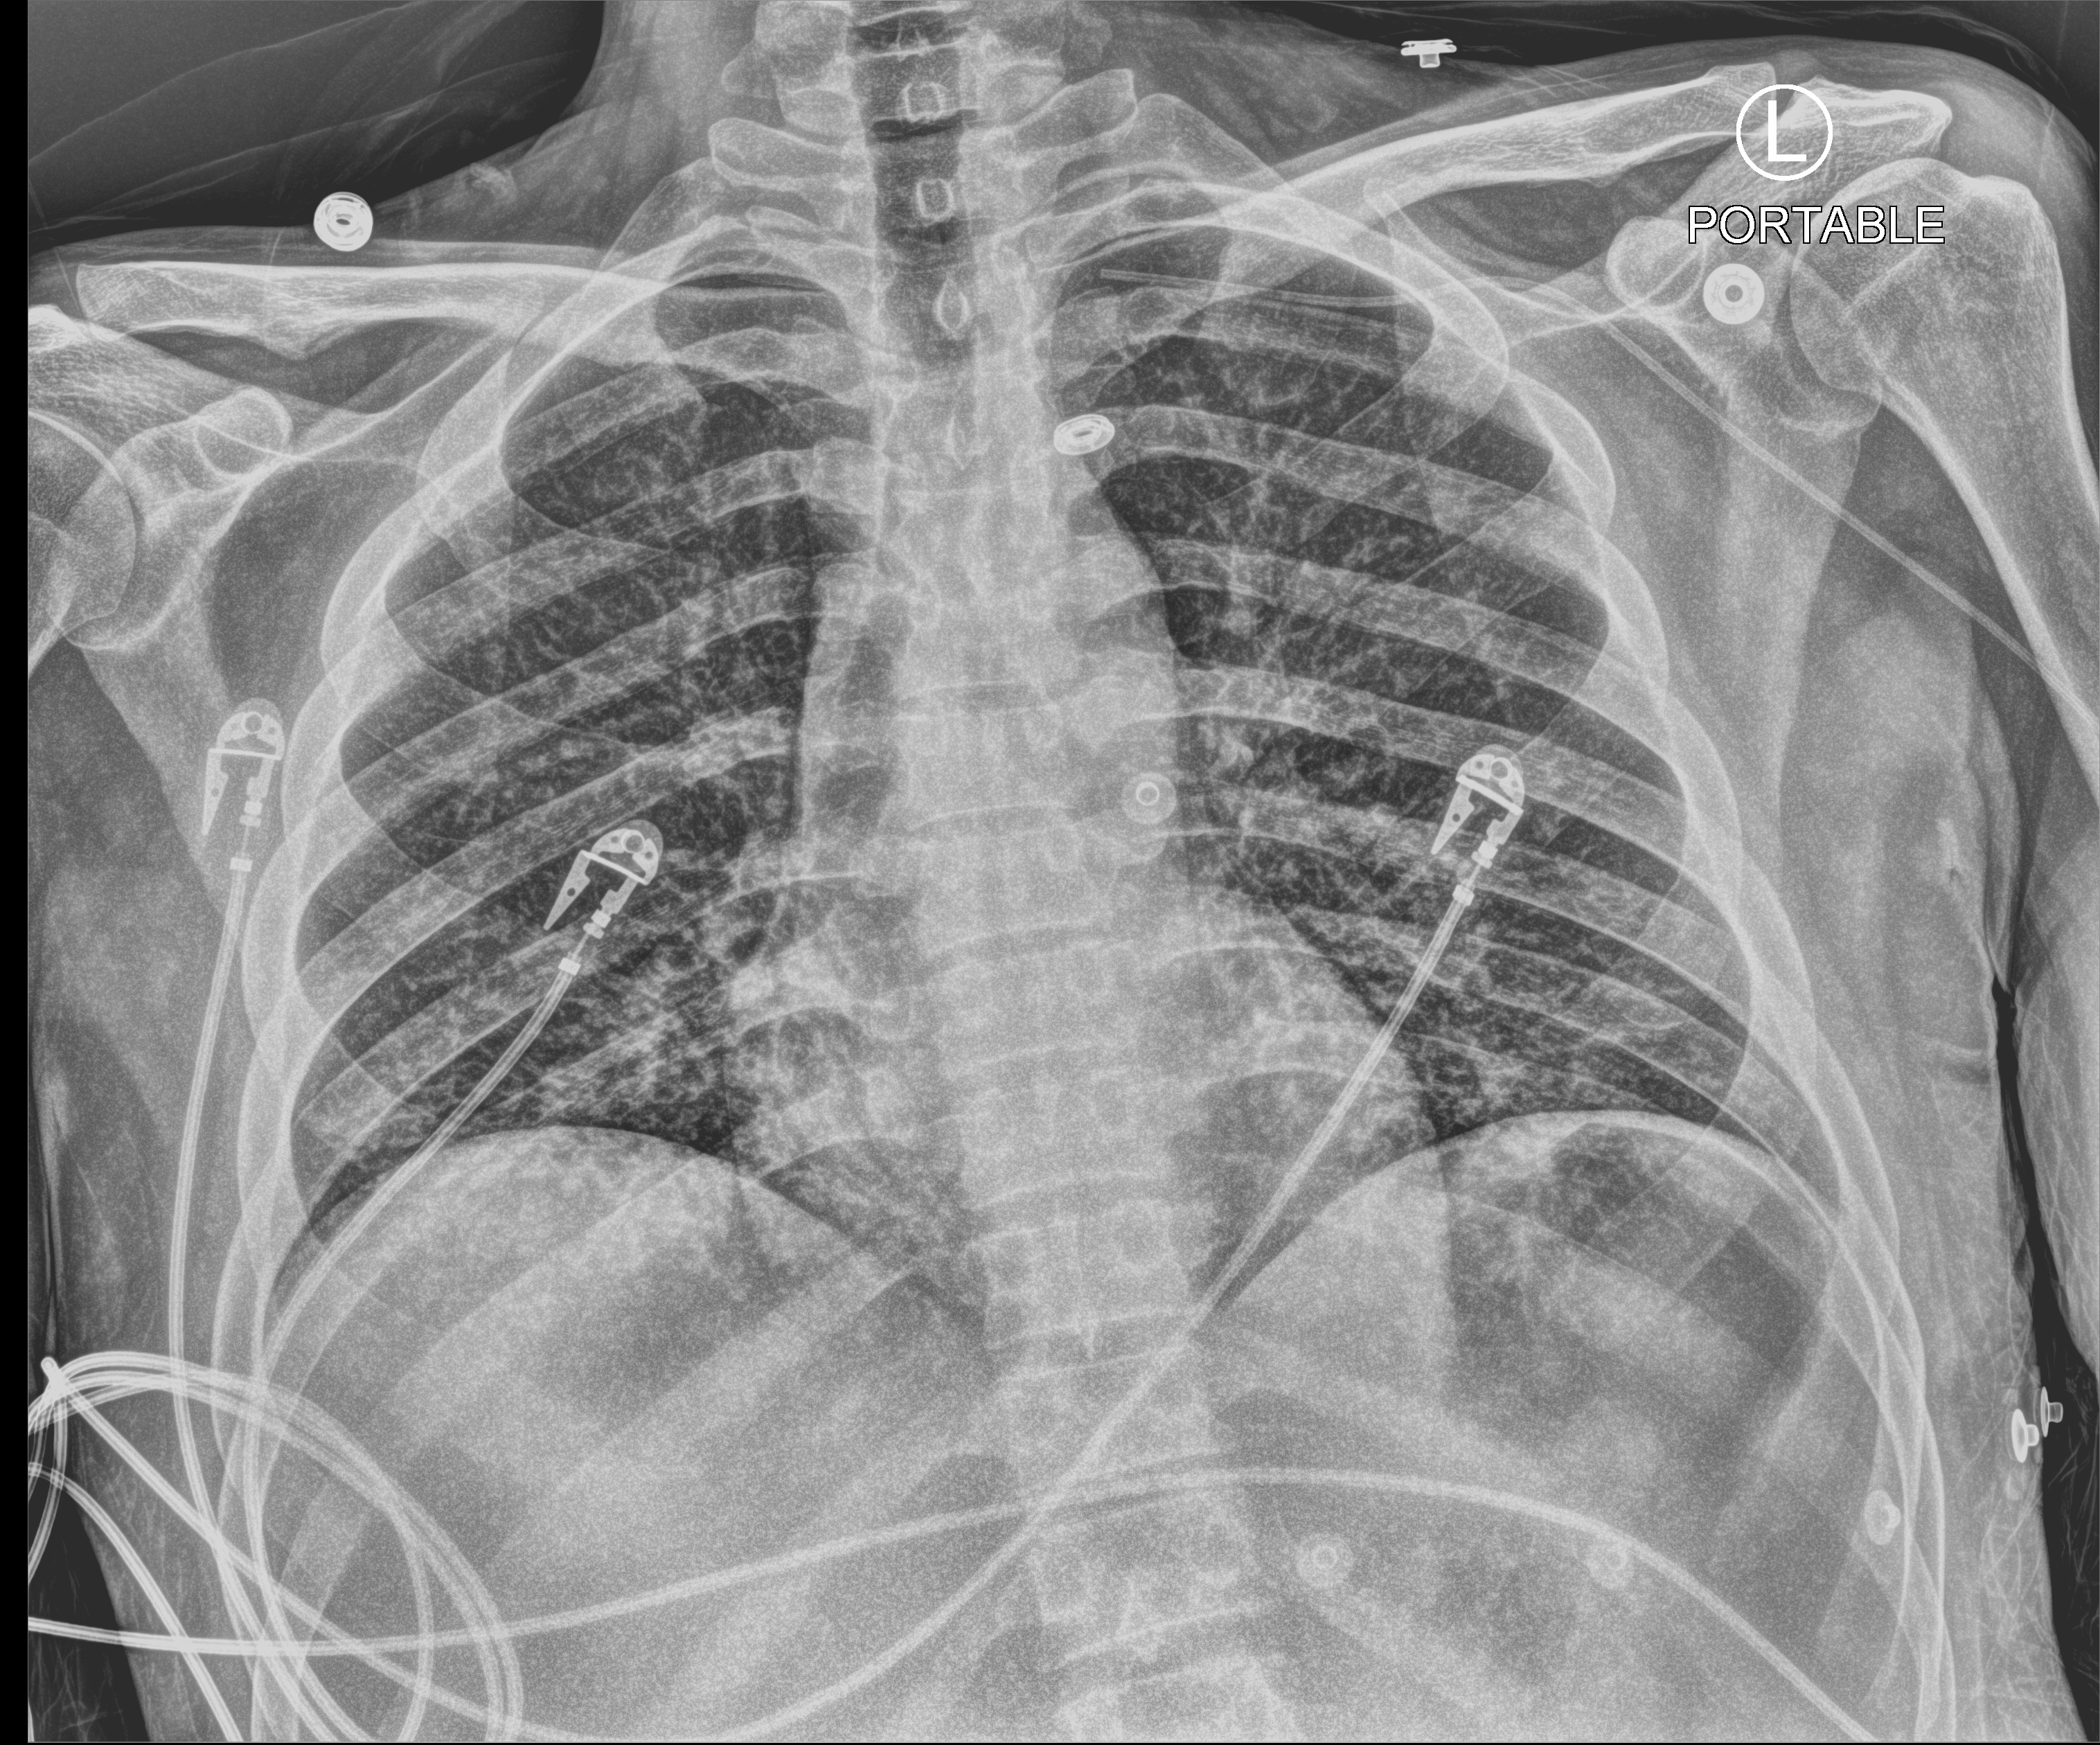
Chest X-ray (portable); anteroposterior (AP) projection. Male patient hospitalised with COVID-19, age 18–59 years.
Hospital-stay facts (about this admission, not read from this image; timing relative to this image not recorded): admitted to intensive care during this hospital stay: yes; mechanically ventilated during this hospital stay: yes; chronic kidney disease (admission record): no.